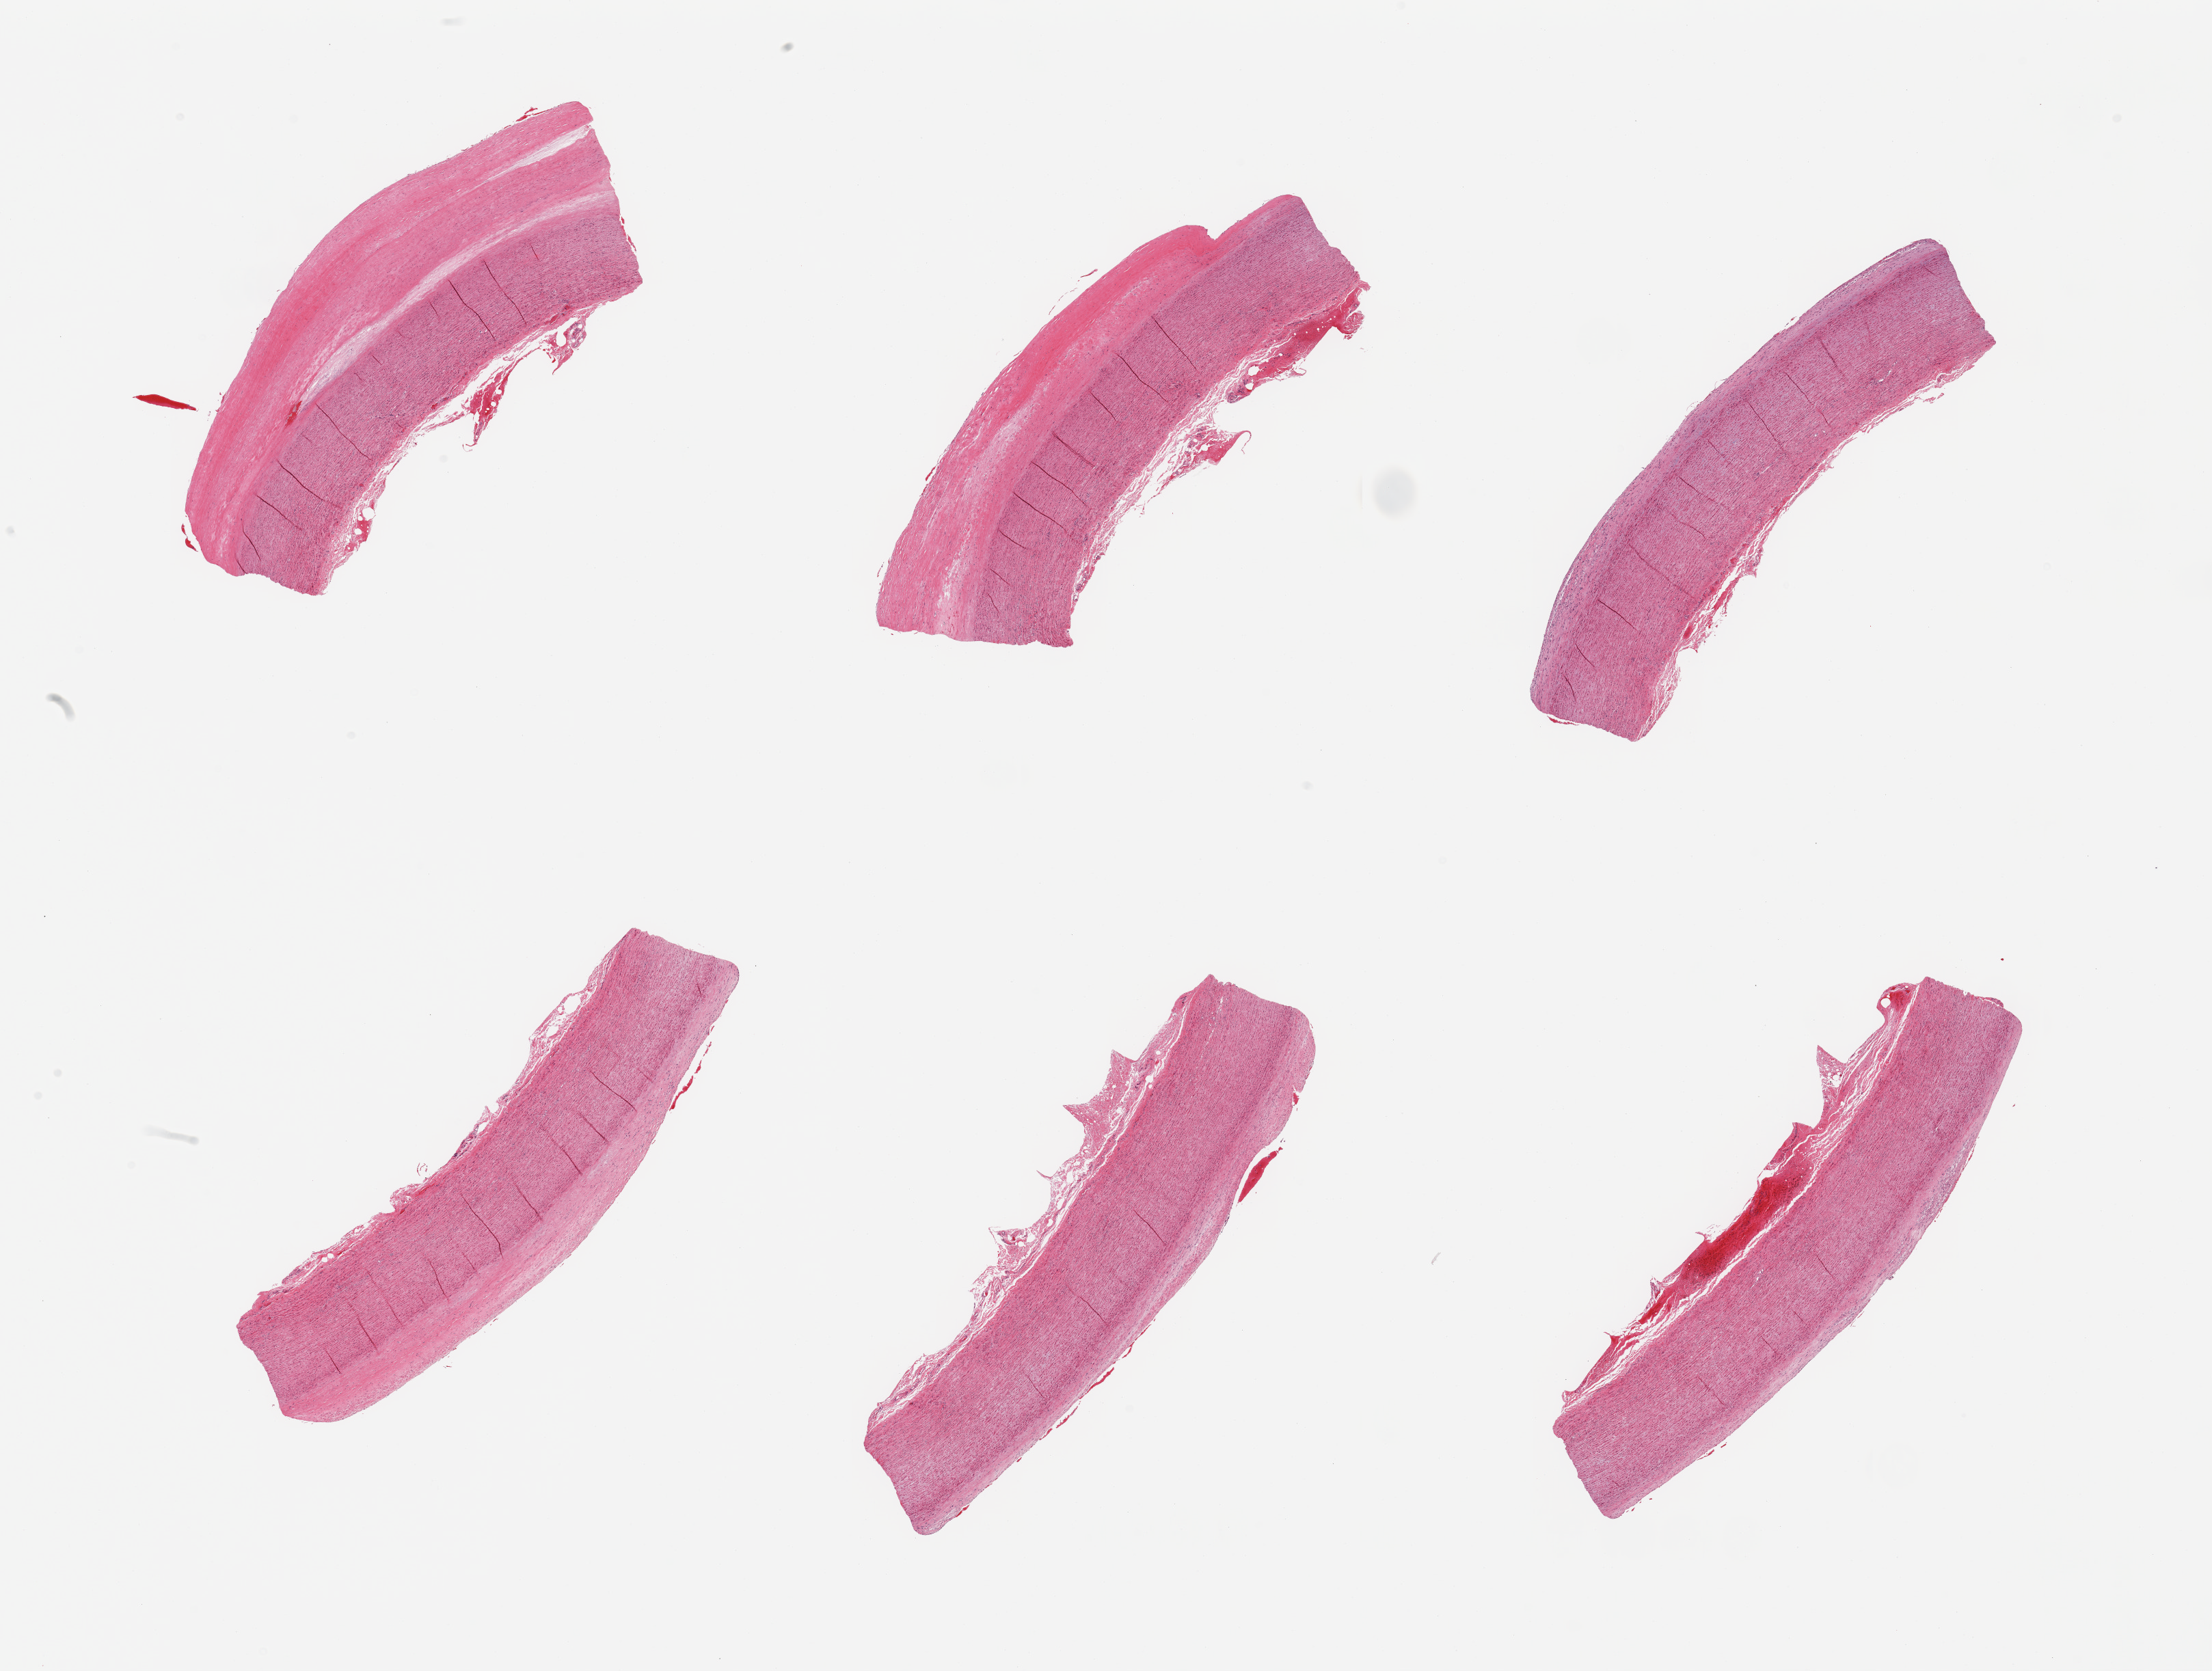
Whole-slide image, haematoxylin and eosin stain — shown as a low-resolution overview of the whole scanned area (about 25.6 x 19.3 mm); PAXgene-fixed, paraffin-embedded tissue; target tissue: aorta; donor tissue sample.
Review note (as recorded): 6 pieces; thick flat intimal plaque up to 1.2 mm.